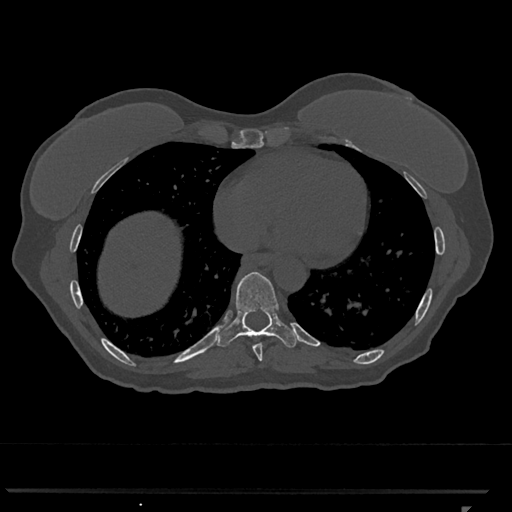
CT including the spine, one axial slice; slice 629 of 793 in the series (ordered by position); reconstruction kernel Br40s/3; bone window (W 1800 / L 400 HU); 0.5 mm slice thickness; 512 × 512 image matrix, field of view 380 × 380 mm. Patient: female, 62 years. From the clinical record (not read from this slice): primary cancer: renal.
Annotated regions visible in this slice (semi-automatic segmentation, software-assisted and operator-edited):
- T8 vertebra: bounding box [x1, y1, x2, y2] px = [253, 343, 263, 362]
- T9 vertebra: [216, 272, 298, 348]